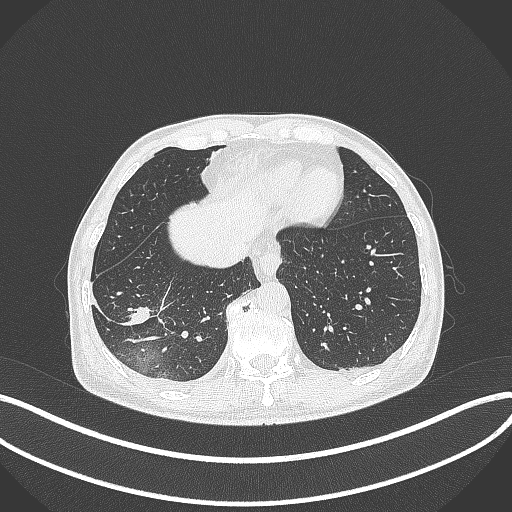
Chest CT, one axial slice; slice 90 of 388 in the series (ordered by position); lung window (W 1500 / L -600 HU); 512 × 512 image matrix, field of view 400 × 400 mm. Patient: male, 64 years. From the clinical record (not read from this slice): clinical TNM (as recorded): T3 N0 M0; histopathological grade: G2-3.
Outlined on this slice (bounding box drawn by a radiologist):
- lung tumour (recorded histology: adenocarcinoma): box from (x=118, y=301) to (x=155, y=334) px